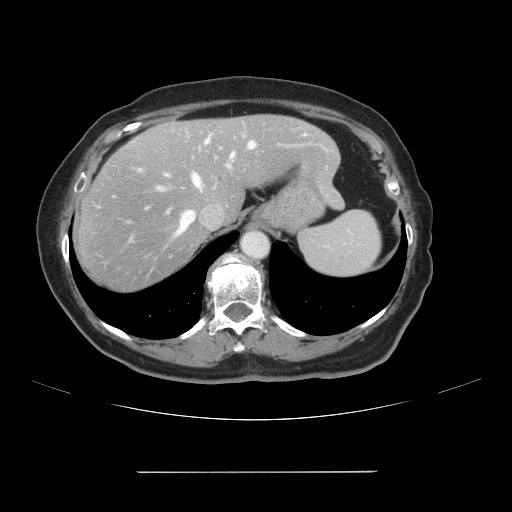
Contrast-enhanced abdominal CT, one axial slice. Slice 82 of 111 in the series (ordered by position). Soft-tissue window (W 400 / L 40 HU). 2.5 mm slice thickness. 512 × 512 image matrix, field of view 400 × 400 mm. Female patient, age 74 years. From the clinical record (not read from this slice): diagnosis: colorectal cancer liver metastases, imaged before liver resection; multiple liver metastases: yes; largest metastasis: 1.1 cm; disease in both lobes: yes.
Annotated regions visible in this slice (outlined manually by an expert reader):
- hepatic veins: bounding box <157,141,255,233> (left, top, right, bottom; pixels)
- liver: <72,115,340,293>
- planned liver remnant (the part of the liver to remain after resection): <162,116,341,220>
- portal vein (with intrahepatic branches): <139,136,231,171>